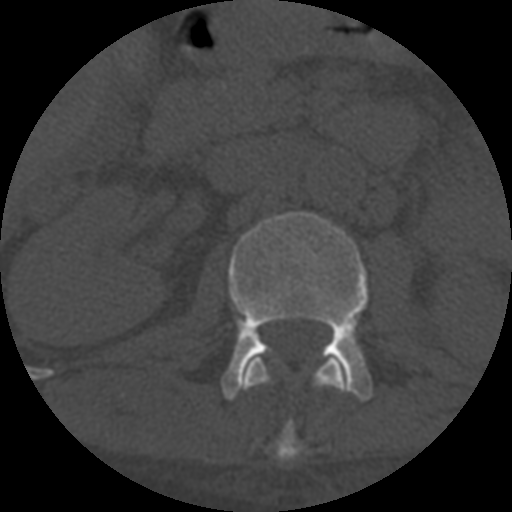
CT including the spine, one axial slice. Slice 270 of 708 in the series (ordered by position). 120 kVp. One of 3 acquisitions stored at this slice position. Bone window (W 1800 / L 400 HU). 512 × 512 image matrix, field of view 160 × 160 mm. Patient age 55 years. Case-level facts recorded for this patient, not image findings: primary cancer: colon; vertebrae with lytic lesions (as recorded): T12, L1, L5.
Outlined on this slice (semi-automatically segmented with operator editing):
- L1 vertebra: bounding box <243,356,347,462> (left, top, right, bottom; pixels)
- L2 vertebra: <221,212,373,401>